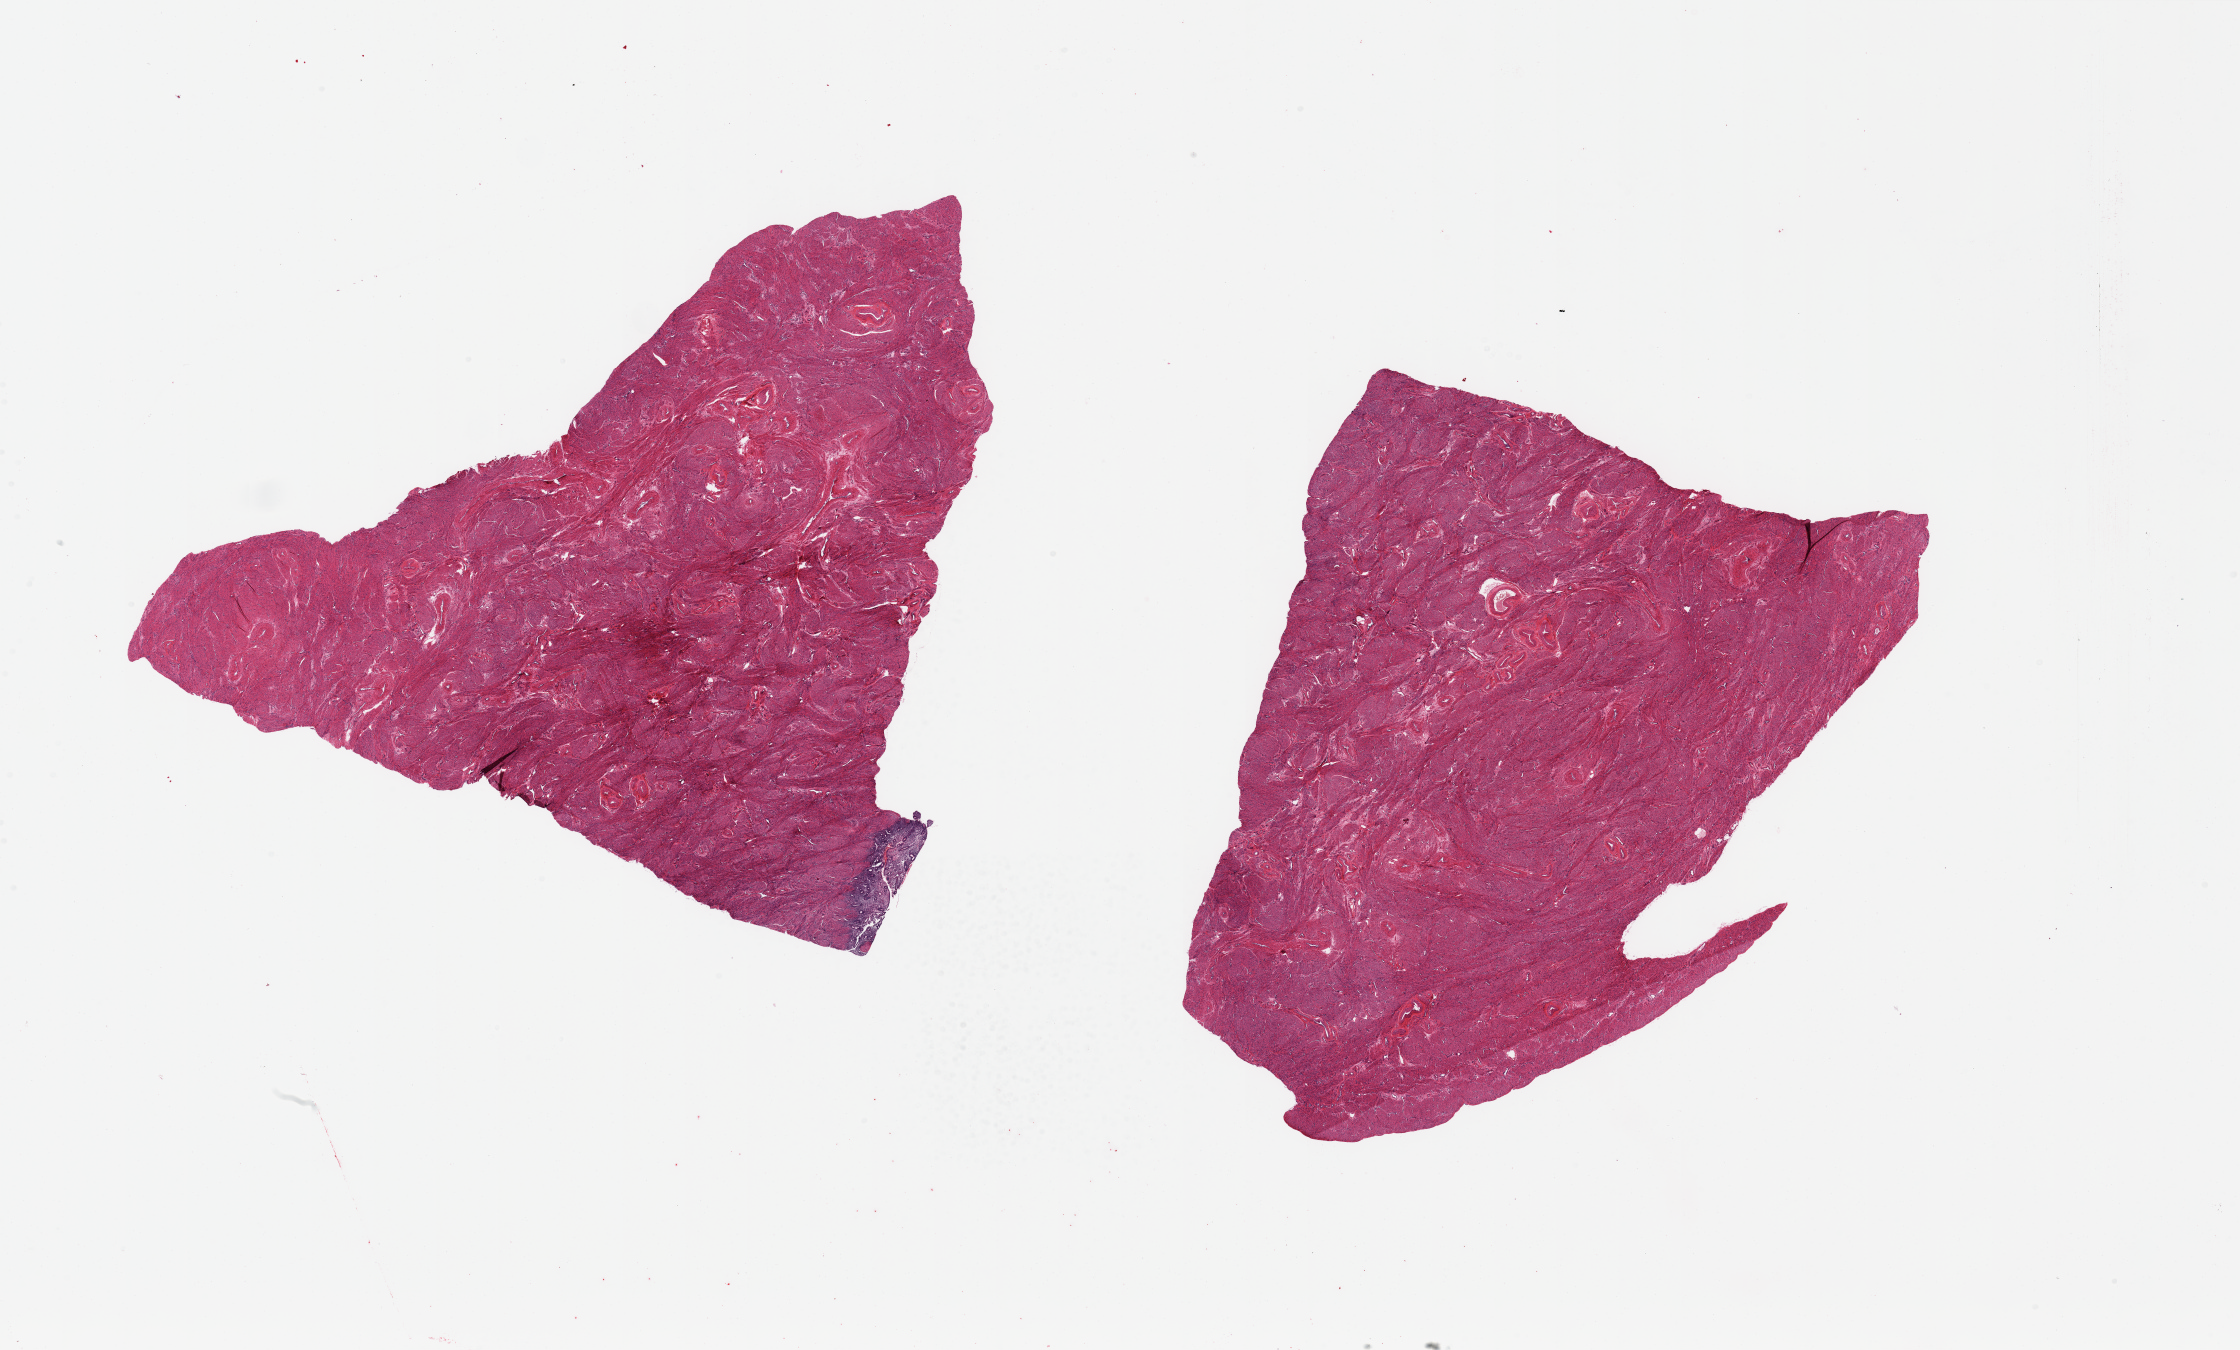
Whole-slide image, hematoxylin and eosin (H&E) stain, brightfield — low-resolution overview of the scanned area, about 35.4 x 21.4 mm, PAXgene-fixed, paraffin-embedded tissue, section of uterus (target tissue), donor tissue sample. Female donor.
Reviewer comment on this tissue sample: 2 pieces, myometrium; trace ~0.5mm nubbin of endometrium.